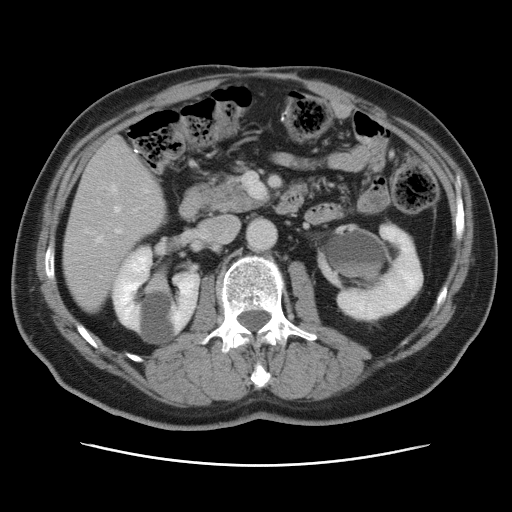
Contrast-enhanced abdominal CT, one axial slice; 120 kVp; intravenous contrast given; soft-tissue window (W 400 / L 40 HU); 5 mm slice thickness; 512 × 512 image matrix. Male patient, age 69 years. From the clinical record (not read from this slice): diagnosis: colorectal cancer liver metastases, imaged before liver resection; multiple liver metastases: no; largest metastasis: 5 cm; disease in both lobes: yes.
Annotated regions visible in this slice (outlined manually by an expert reader):
- hepatic veins: bounding box (x1, y1, x2, y2) in pixels: (96, 185, 119, 243)
- liver: (64, 137, 165, 310)
- planned liver remnant (the part of the liver to remain after resection): (64, 214, 142, 310)
- portal vein (with intrahepatic branches): (115, 228, 122, 234)